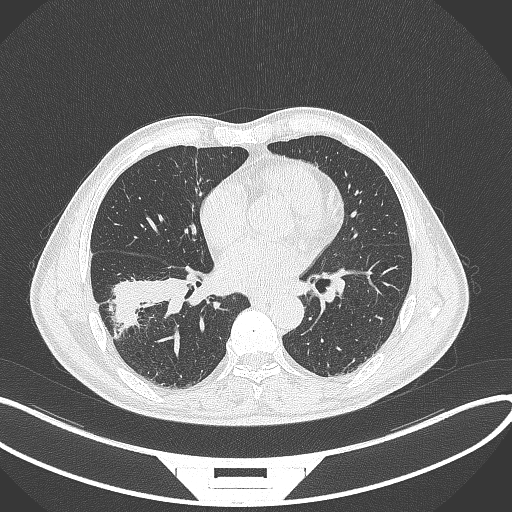
Chest CT, one axial slice; slice 161 of 364 in the series (ordered by position); reconstruction kernel B70f; 120 kVp; lung window (W 1500 / L -600 HU); 512 × 512 image matrix, field of view 400 × 400 mm. Male patient, age 58 years. From the clinical record (not read from this slice): clinical TNM (as recorded): T3 N0 M0; histopathological grade: G2.
Structures marked on this image (rectangle marked by the reading radiologist):
- lung tumour (recorded histology: squamous cell carcinoma): bounding box <105,276,187,332> (left, top, right, bottom; pixels)